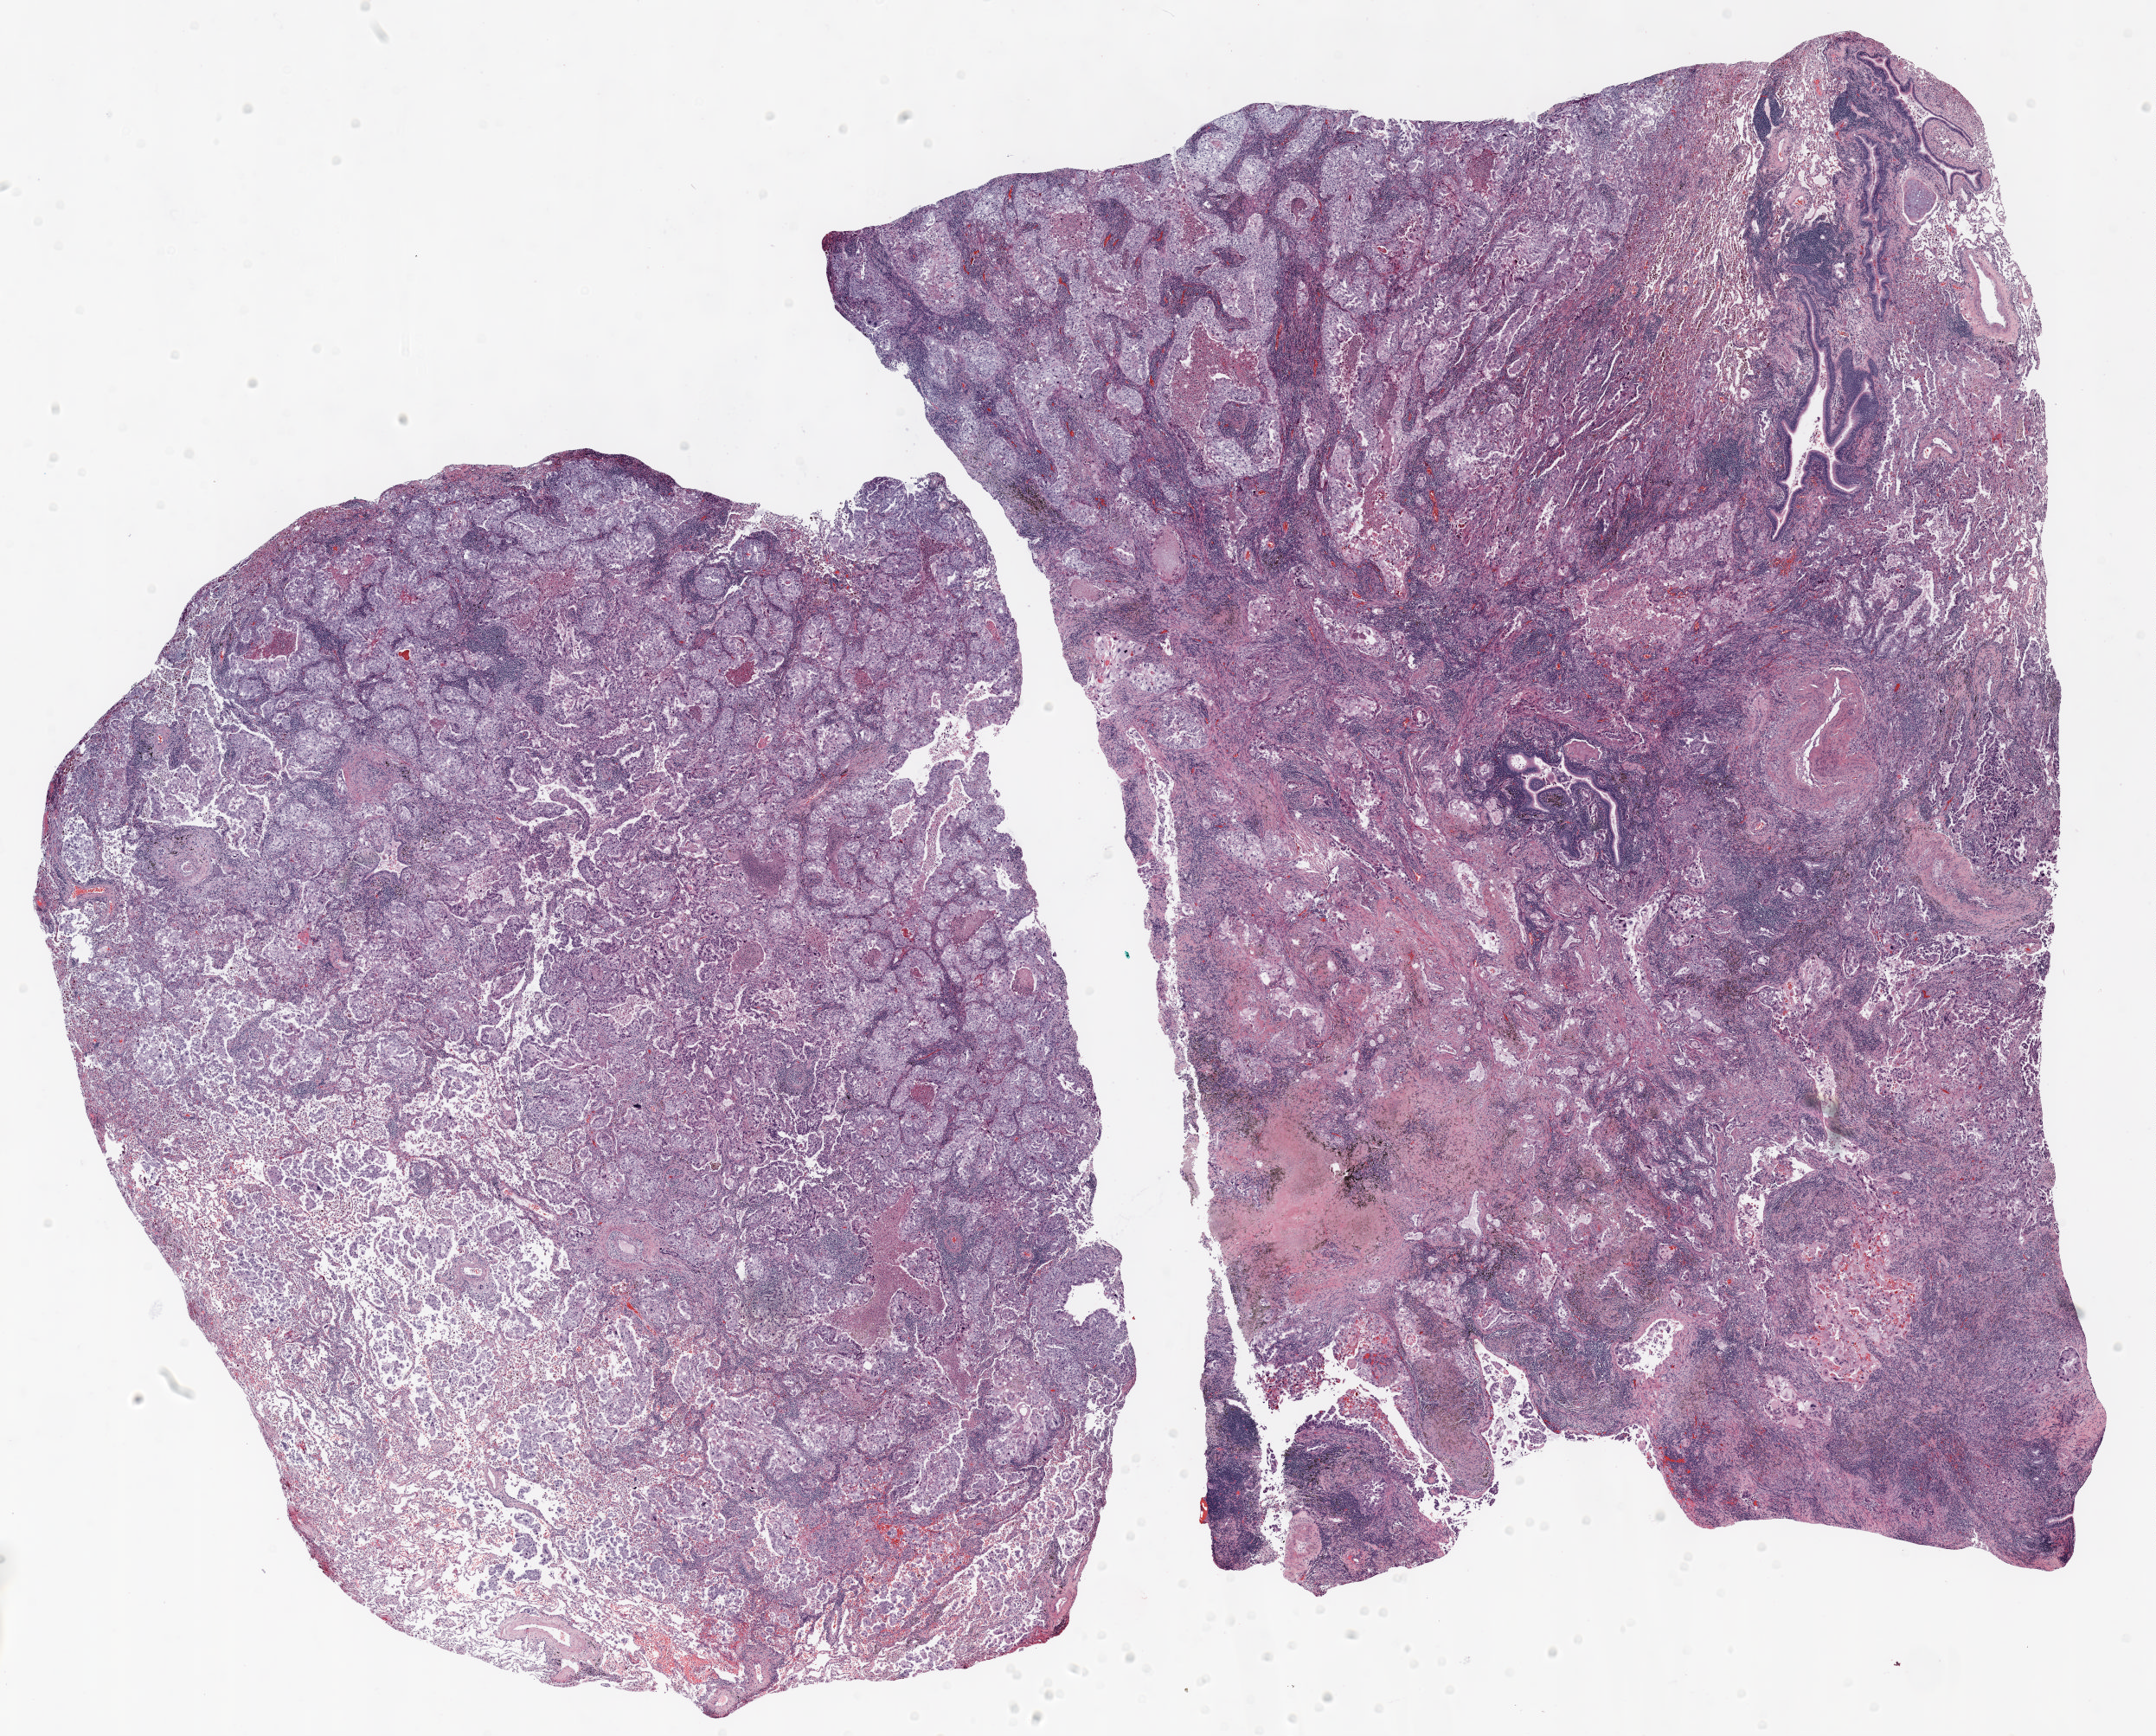
Whole-slide histology image, H&E, whole scanned area (about 20.0 x 16.1 mm) shown as a low-resolution overview; formalin-fixed paraffin-embedded (FFPE) section; lung. Male, age 66 at enrolment. Current smoker at enrolment. Grade: poorly differentiated (G3).
• tumour size (pathology): 50 mm
• participant's lung-cancer diagnosis: Squamous cell carcinoma, adenoid
• stage (AJCC 6th edition): IIB
• primary tumour location (clinical record): right upper lobe